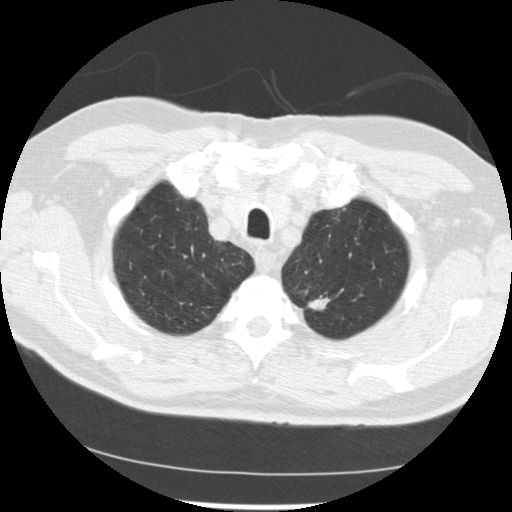
Low-dose screening chest CT, one axial slice. Reconstruction kernel STANDARD. 120 kVp. Lung window (W 1500 / L -600 HU). 2.5 mm slice thickness. 512 × 512 image matrix, field of view 341 × 341 mm.
Outlined on this slice (expert manual segmentation):
- lesion 2 (tumor, upper lobe of left lung): bounding box <308,297,329,310> (left, top, right, bottom; pixels)